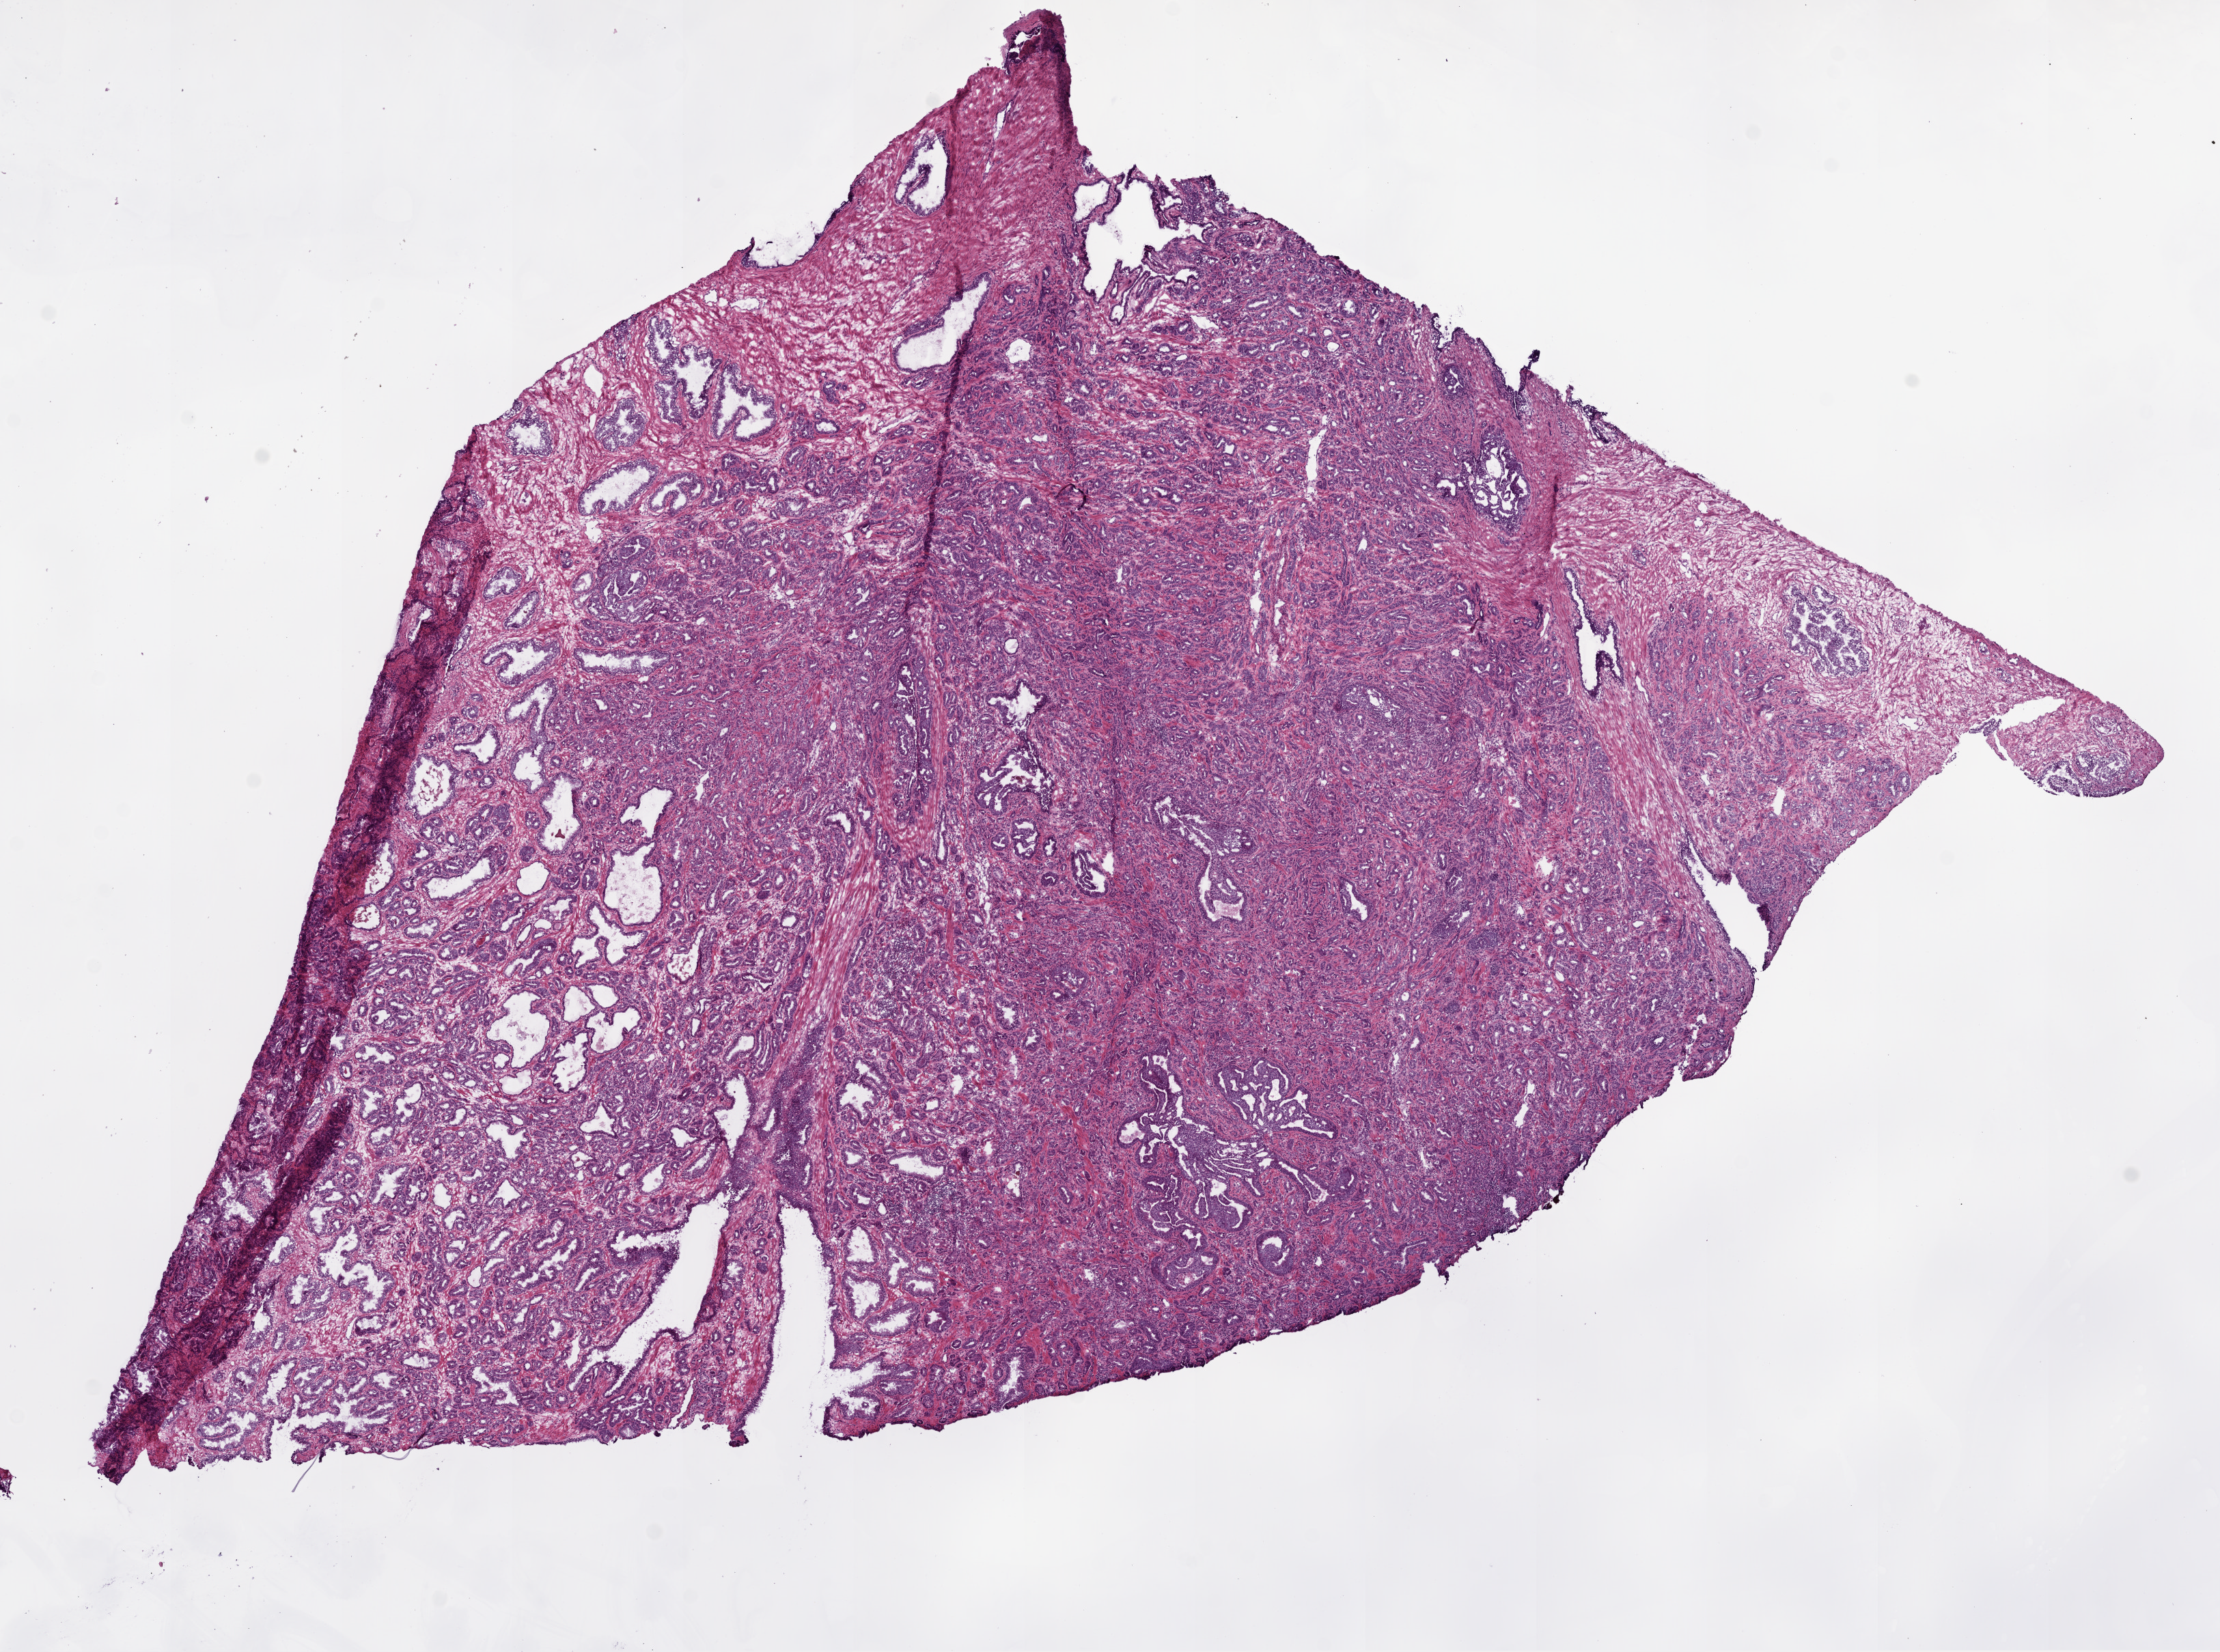
Hematoxylin and eosin (H&E) stained whole-slide image — shown as a low-resolution overview of the whole scanned area (about 13.0 x 9.7 mm, acquisition: 20x scan); frozen section from the top of the tissue portion; prostate, primary tumour sample. Patient: male, age at initial diagnosis 48 years. Gleason score: 7 (4+3). Slide review estimates, as recorded: tumour cells 75%, tumour nuclei 75%, normal cells 15%, stromal cells 10%, necrosis 0%. Infiltration values recorded for this section: lymphocyte infiltration 0%, monocyte infiltration 0%, neutrophil infiltration 0%.
Histologic diagnosis: Acinar cell carcinoma.